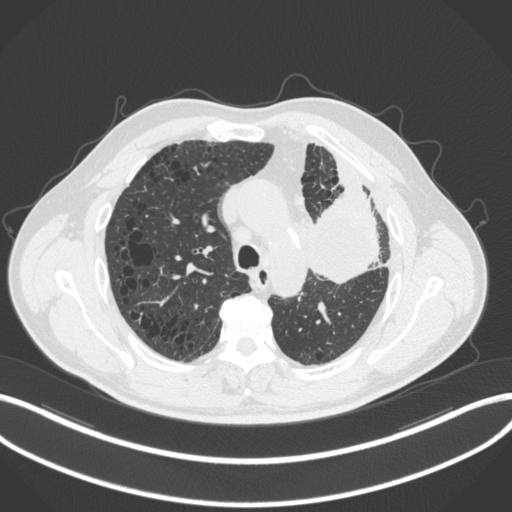
Chest CT, one axial slice. Slice 208 of 286 in the series (ordered by position). 120 kVp. Lung window (W 1500 / L -600 HU). 1 mm slice thickness. 512 × 512 image matrix. Patient: male, 68 years. Case-level facts recorded for this patient, not image findings: clinical TNM (as recorded): T3 N3 M1.
Annotated regions visible in this slice (bounding box drawn by a radiologist):
- lung tumour (recorded histology: adenocarcinoma): bounding box <301,176,384,289> (left, top, right, bottom; pixels)